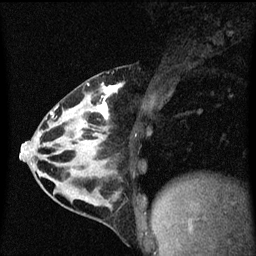
Breast MRI (dynamic contrast-enhanced), one sagittal slice. Slice 27 of 60 in the series (ordered by position). Dynamic contrast-enhanced series, image 2 of 3 at this slice position (ordered by acquisition). 1.5 T. TE 4.2 ms, TR 8.4 ms. 2 mm slice thickness. 256 × 256 image matrix, field of view 200 × 200 mm. Patient: female, 32 years.
Outlined on this slice (semi-automatic segmentation, software-assisted and operator-edited):
- analysis volume of interest (the breast-tissue region the enhancement analysis was run in; not a lesion): bounding box <34,74,141,169> (left, top, right, bottom; pixels)
- tumour enhancement mask (voxels above the 70 % enhancement threshold inside the analysis volume of interest): <51,84,123,121>